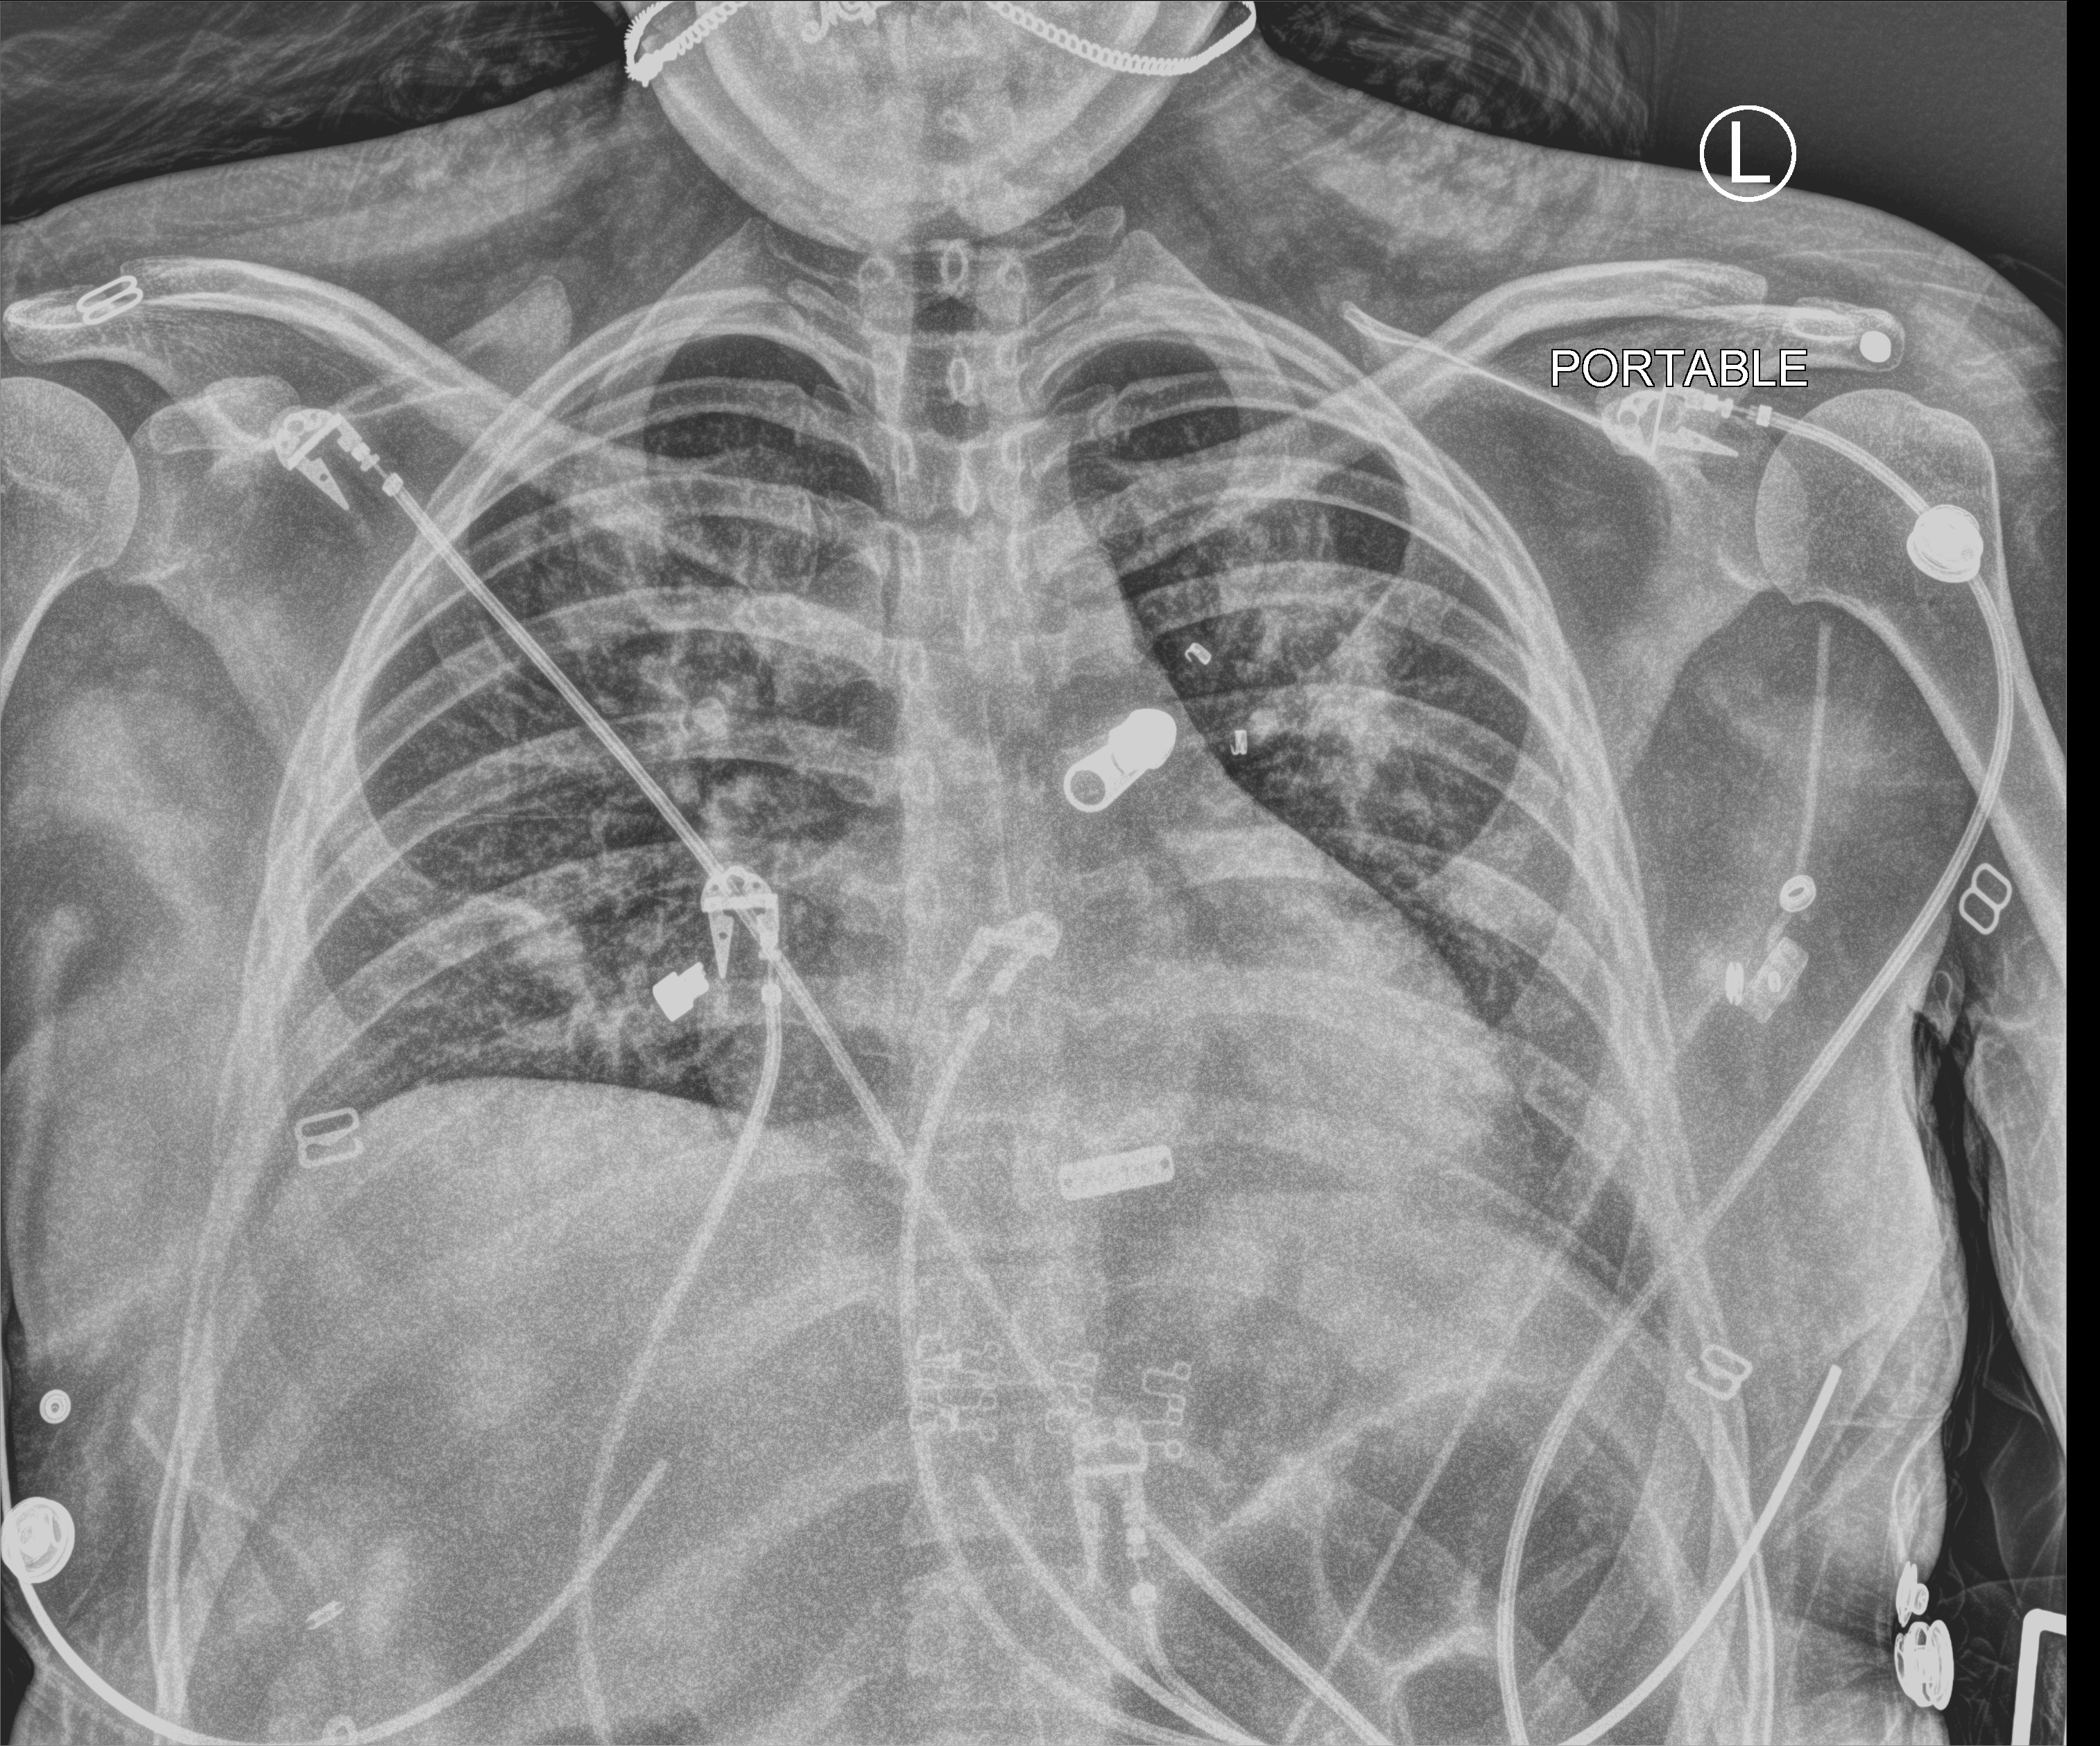
Bedside chest radiograph (computed radiography). Patient hospitalised with COVID-19; female, aged 18–59 years.
Hospital-stay facts (about this admission, not read from this image; timing relative to this image not recorded): mechanically ventilated during this hospital stay: no; length of hospital stay: 2 days.